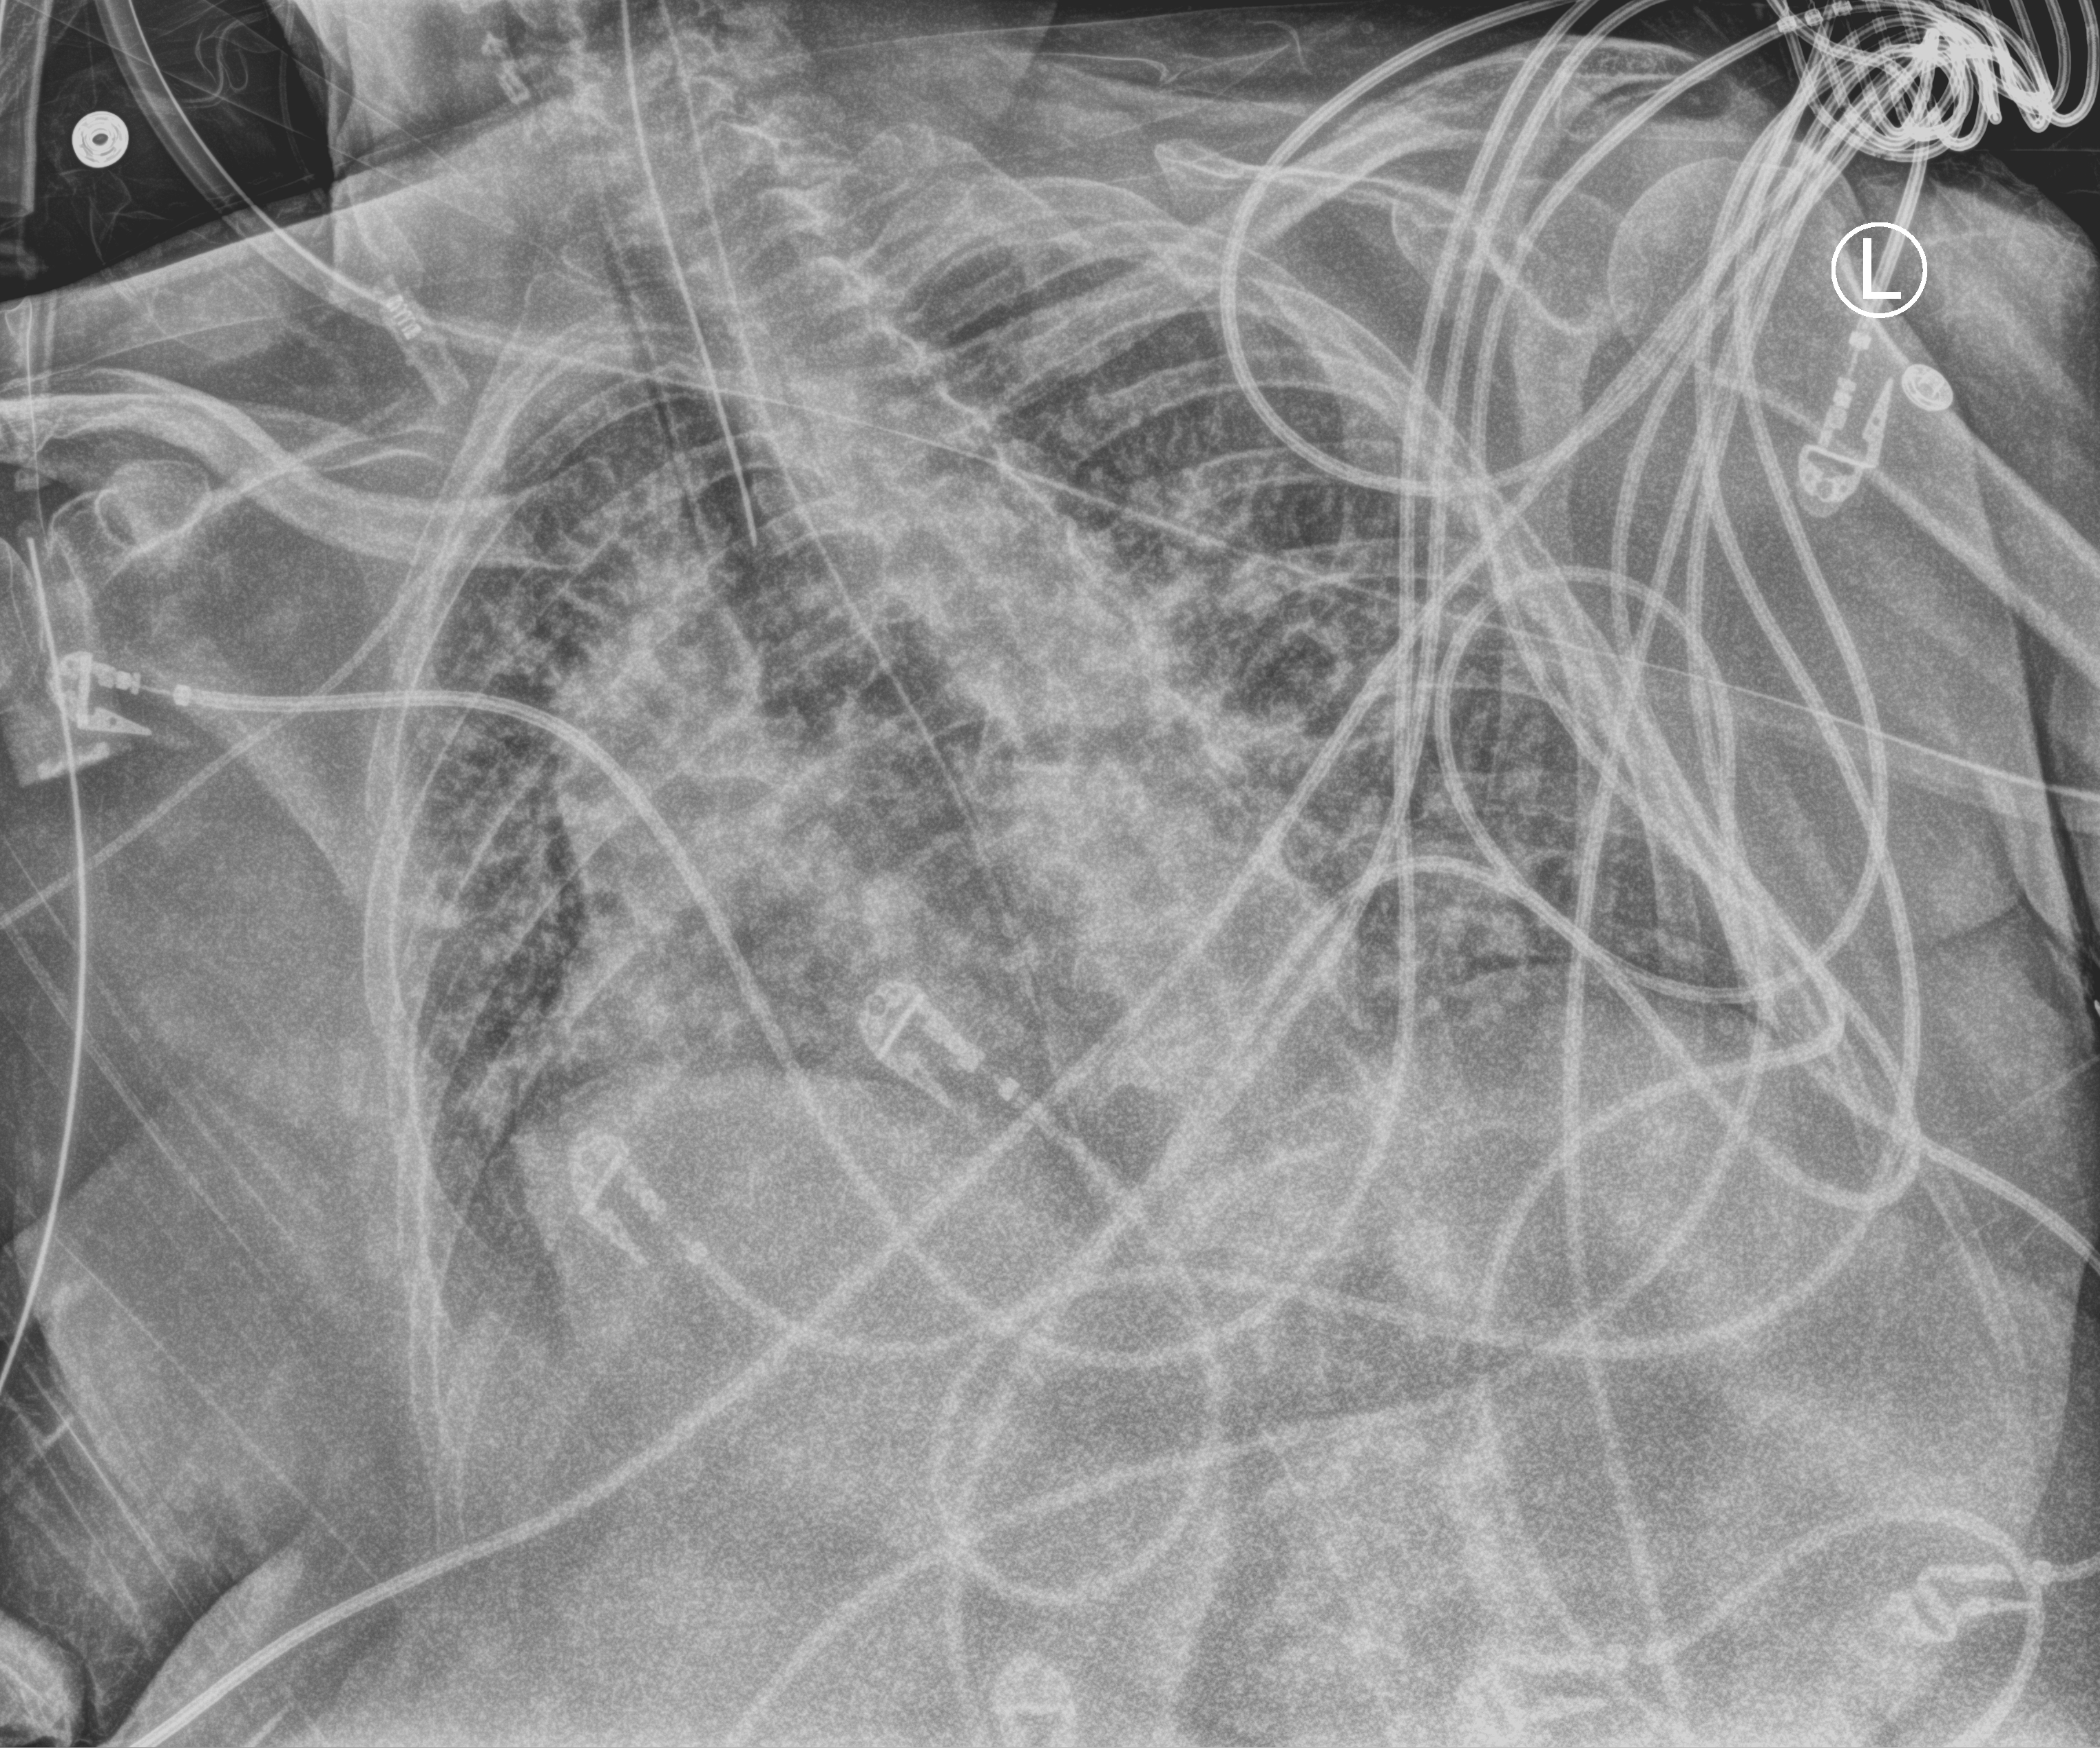
Chest X-ray (portable); anteroposterior (AP) projection. Female patient hospitalised with COVID-19, age 75–90 years.
From the hospital-stay record, not from the radiograph (when in the stay this image was taken is not recorded): mechanically ventilated during this hospital stay: yes.